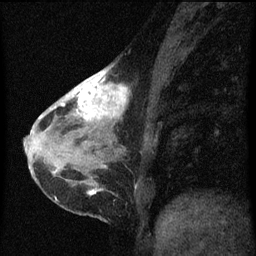
Breast MRI (dynamic contrast-enhanced), one sagittal slice. Slice 24 of 60 in the series (ordered by position). Dynamic contrast-enhanced series, image 2 of 3 at this slice position (ordered by acquisition). 1.5 T. TE 4.2 ms, TR 8 ms. 256 × 256 image matrix. Patient: female, 38 years.
Outlined on this slice (semi-automatic segmentation, software-assisted and operator-edited):
- analysis volume of interest (the breast-tissue region the enhancement analysis was run in; not a lesion): bounding box [x1, y1, x2, y2] px = [61, 66, 130, 147]
- tumour enhancement mask (voxels above the 70 % enhancement threshold inside the analysis volume of interest): [61, 68, 130, 121]